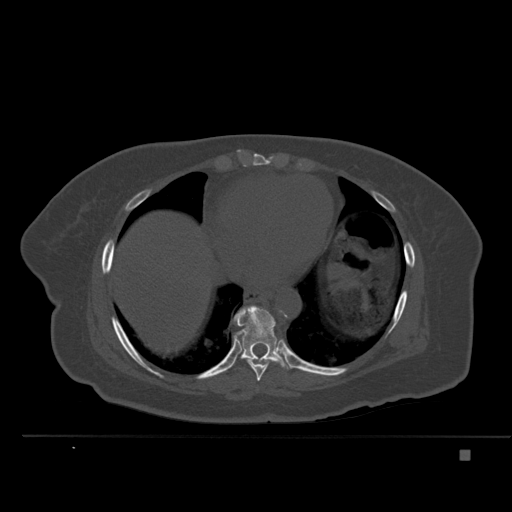
CT including the spine, one axial slice. Position 303 of 477 along the scan axis. Bone window (W 1800 / L 400 HU). 1.5 mm slice thickness. 512 × 512 image matrix, field of view 422 × 422 mm. Patient: female, 74 years. Case-level facts recorded for this patient, not image findings: primary cancer: colon.
Structures marked on this image (semi-automatically segmented with operator editing):
- T8 vertebra: bounding box [x1, y1, x2, y2] px = [247, 359, 268, 381]
- T9 vertebra: [234, 305, 291, 369]